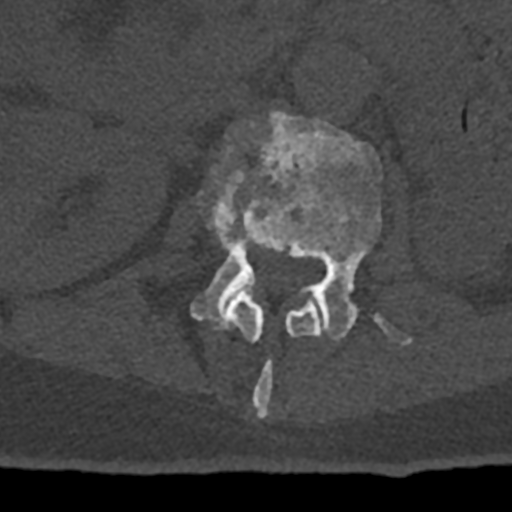
CT including the spine, one axial slice. Position 401 of 797 along the scan axis. 120 kVp. Bone window (W 1800 / L 400 HU). 0.5 mm slice thickness. 512 × 512 image matrix, field of view 160 × 160 mm. Patient: male, 74 years. From the clinical record (not read from this slice): primary cancer: renal; vertebrae with lytic lesions (as recorded): T10, L1, L2, L3, L4, L5.
Outlined on this slice (semi-automatically segmented with operator editing):
- L1 vertebra: box from (x=203, y=146) to (x=321, y=417) px
- L2 vertebra: (x=190, y=111)–(x=412, y=345)